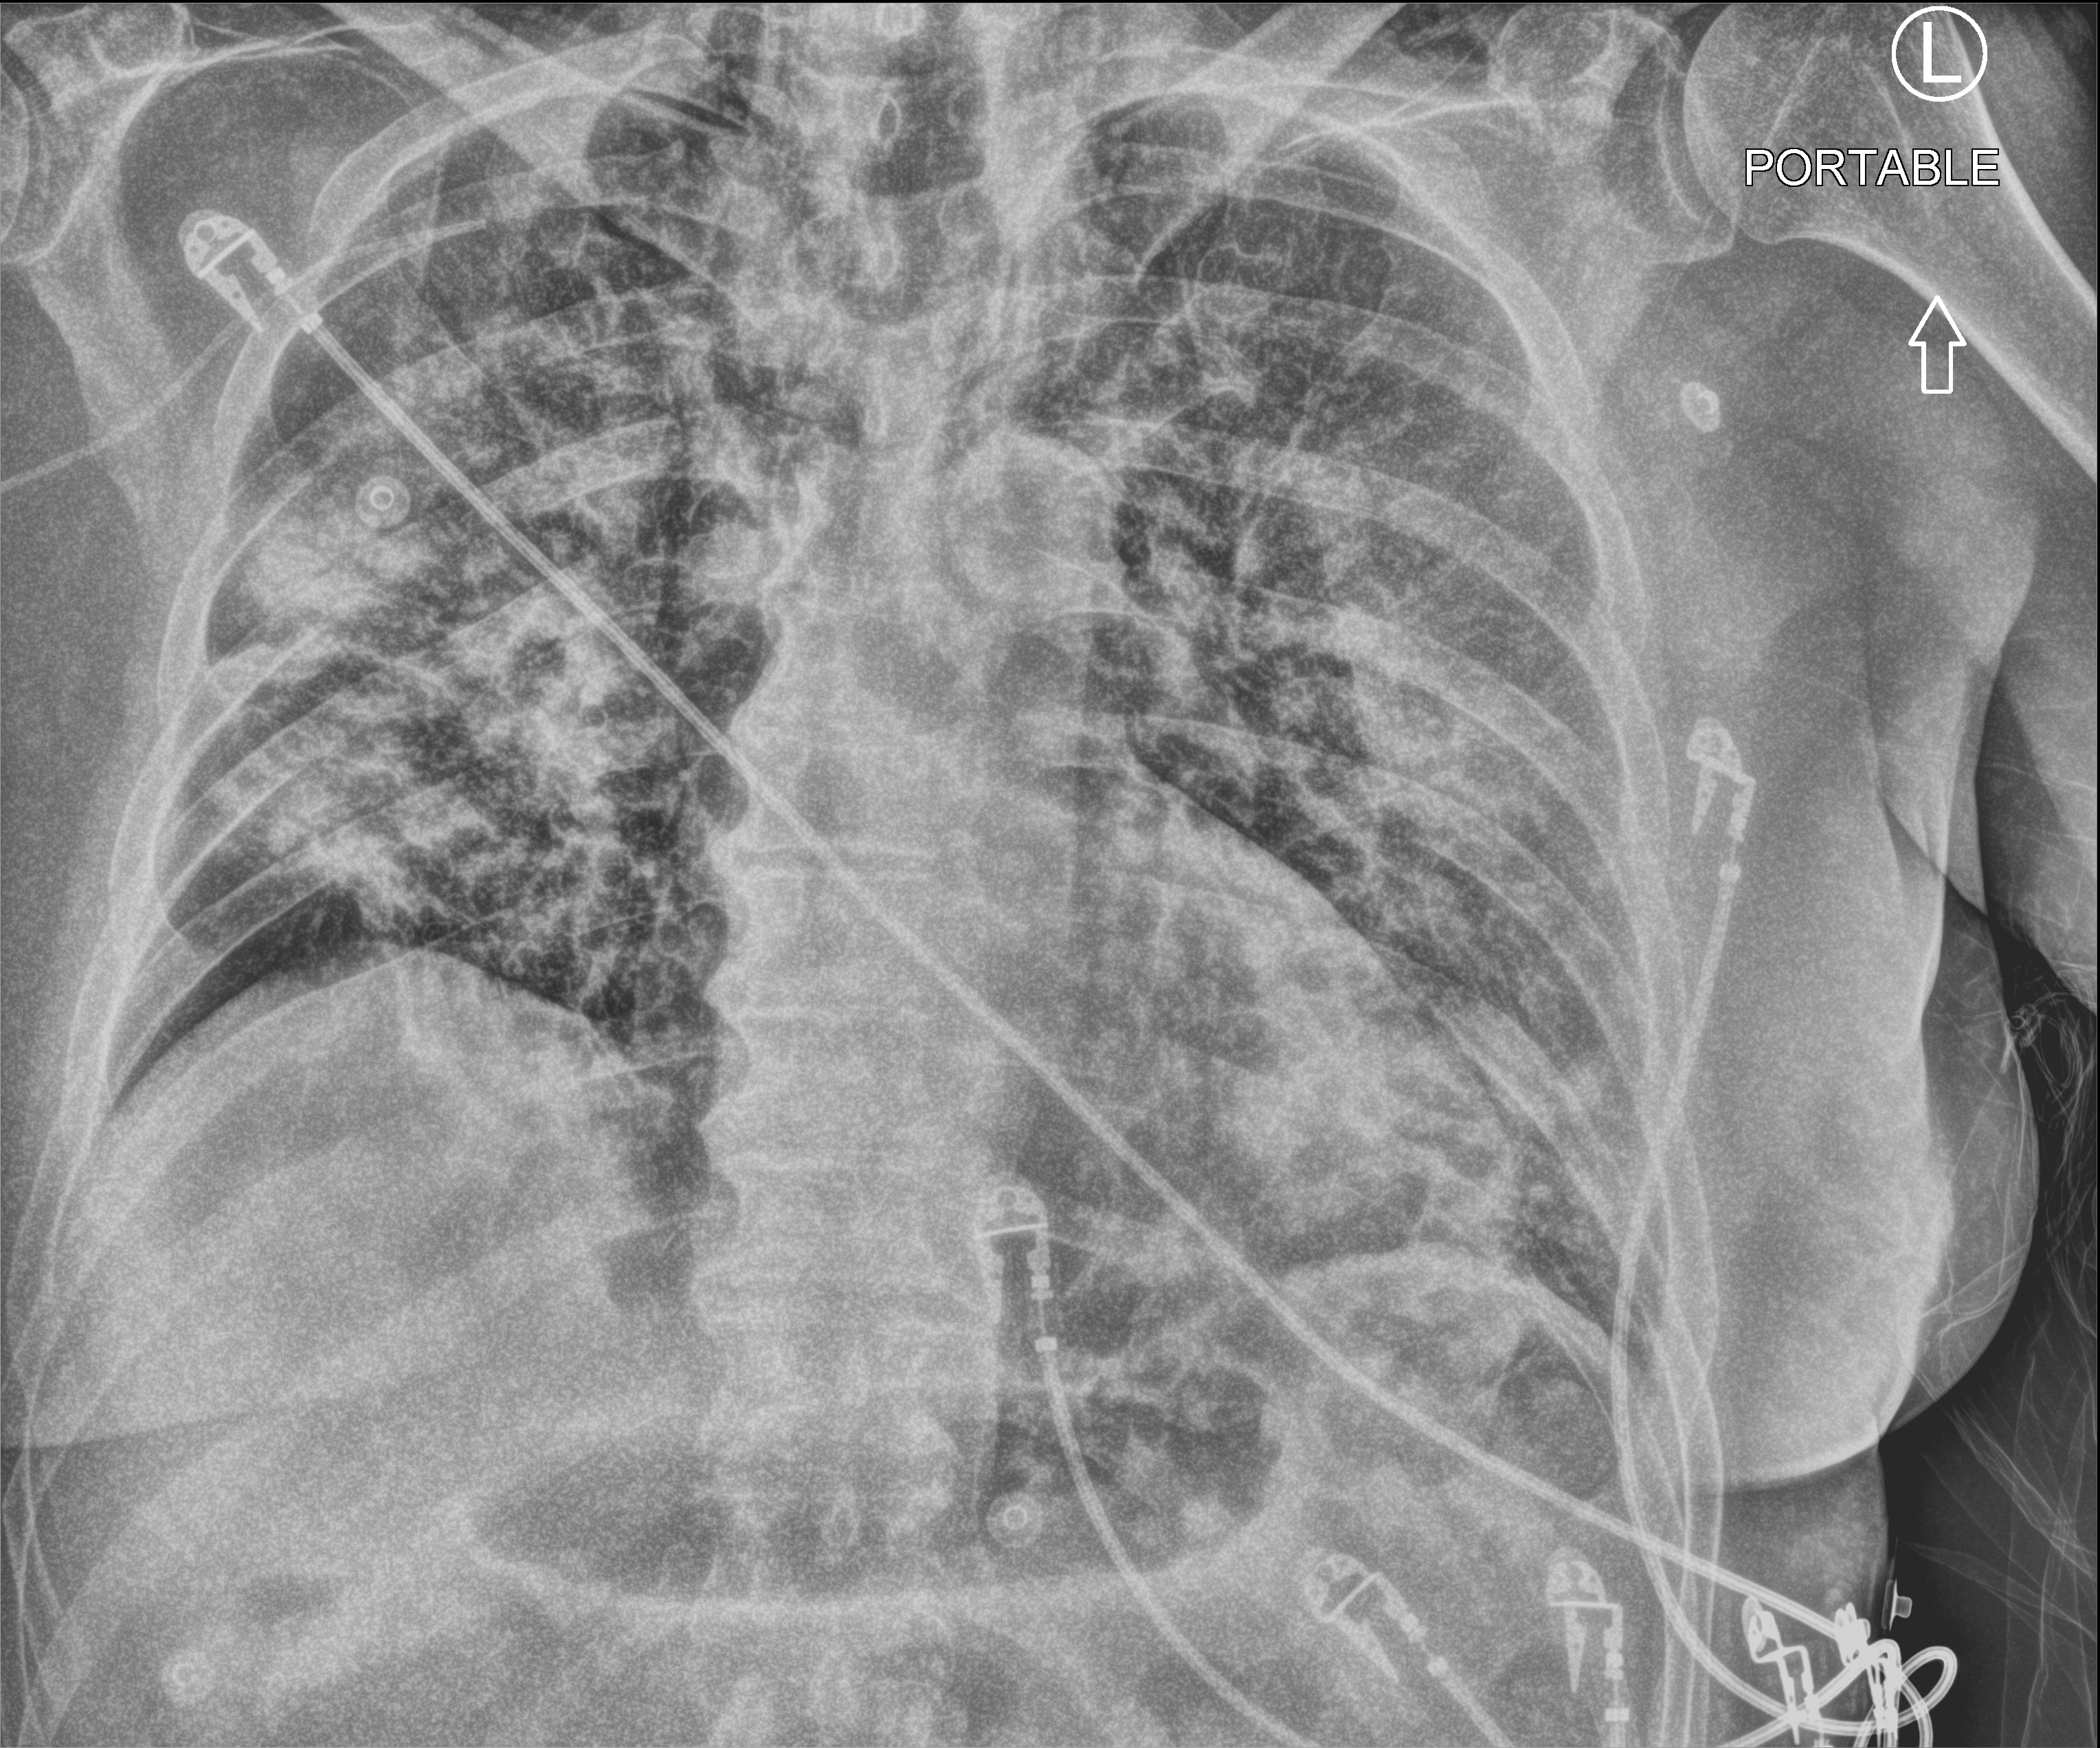
Bedside chest radiograph (computed radiography); anteroposterior (AP) projection. Male patient hospitalised with COVID-19, age 60–74 years.
Hospital-stay facts (about this admission, not read from this image; timing relative to this image not recorded): admitted to intensive care during this hospital stay: no; mechanically ventilated during this hospital stay: no.